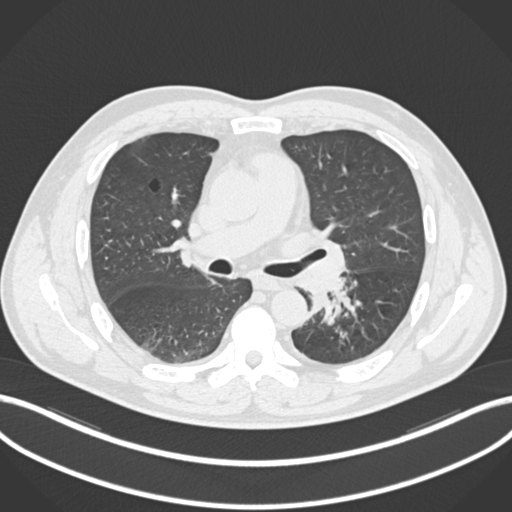
Chest CT, one axial slice. Position 133 of 223 along the scan axis. Reconstruction kernel B30f. 120 kVp. Lung window (W 1500 / L -600 HU). 512 × 512 image matrix, field of view 400 × 400 mm. Patient: male, 50 years. Case-level facts recorded for this patient, not image findings: clinical TNM (as recorded): T2a N3 M0.
Annotated regions visible in this slice (bounding box drawn by a radiologist):
- lung tumour (recorded histology: squamous cell carcinoma): bounding box [x1, y1, x2, y2] px = [306, 278, 358, 326]